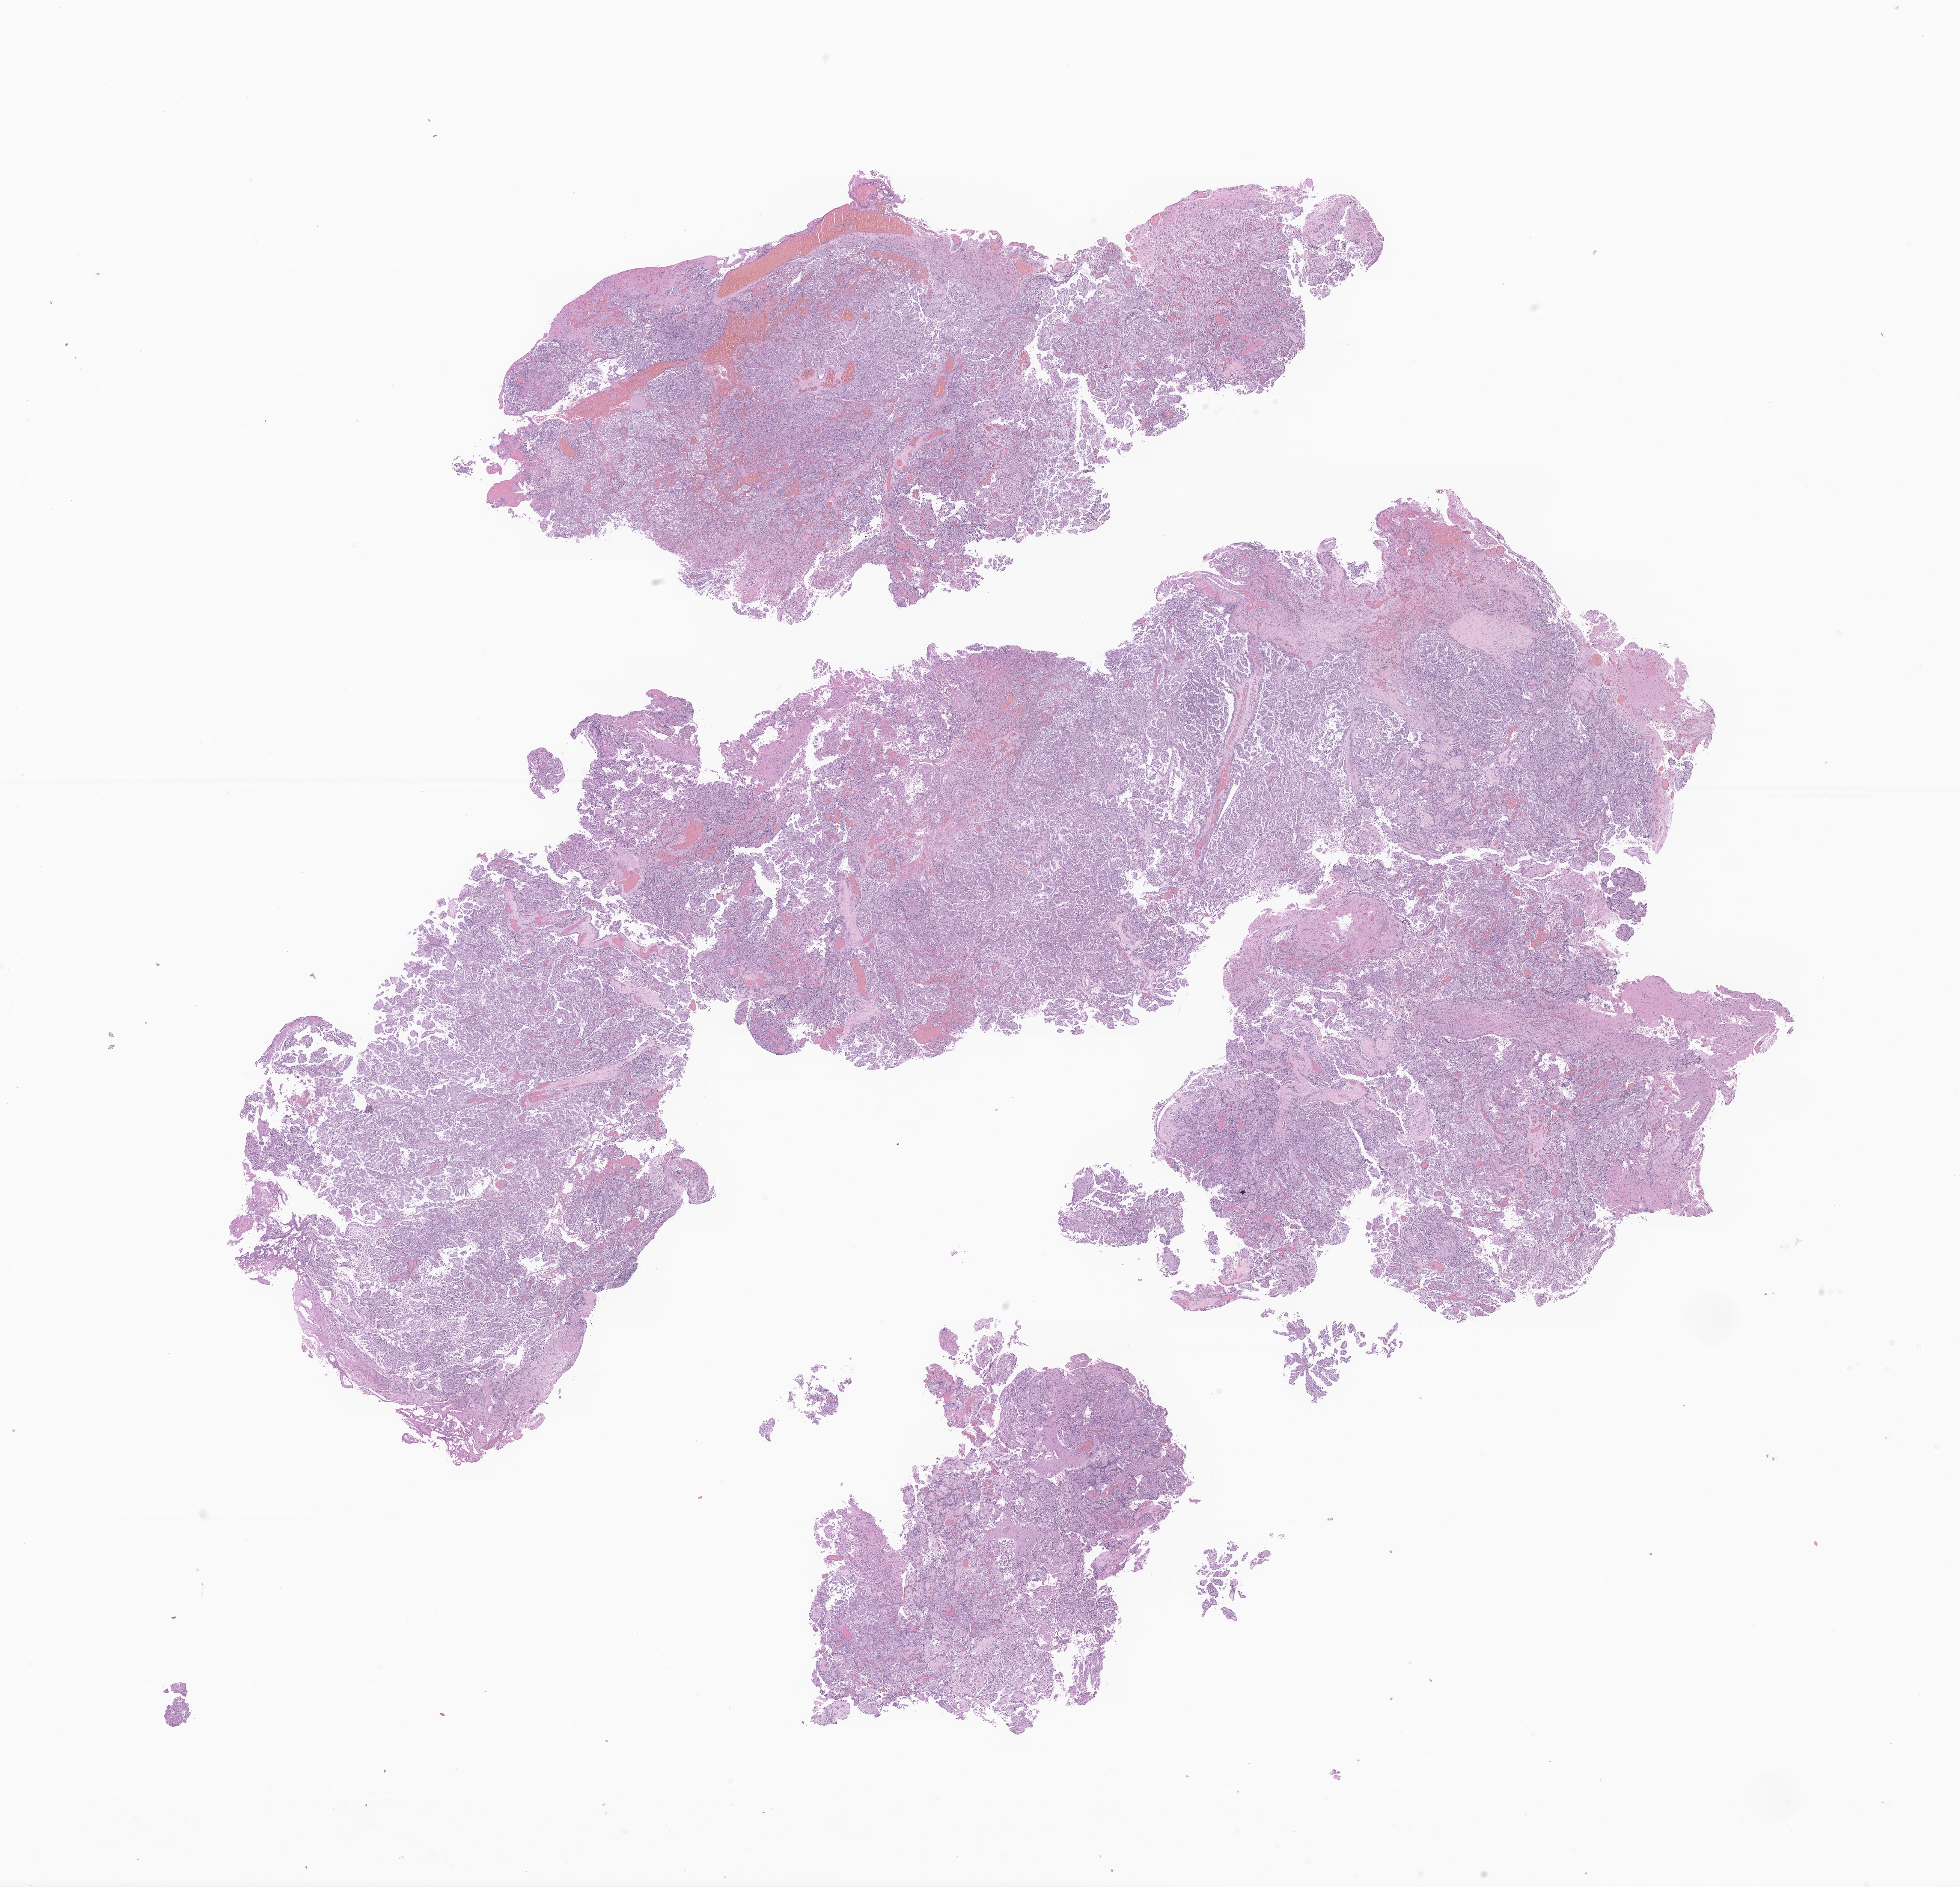
Digitized haematoxylin and eosin-stained section of tumor tissue from the cerebral ventricle — whole scanned area (about 22.0 x 21.2 mm) shown as a low-resolution overview; FFPE section. Patient: male, age 459 days (about 1.3 years).
* diagnosis: Choroid plexus carcinoma